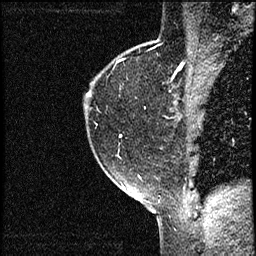
Breast MRI (dynamic contrast-enhanced), one sagittal slice. Slice 44 of 56 in the series (ordered by position). Dynamic contrast-enhanced study with each time point stored as its own series, time point 2 of 3 at this slice position (early post-contrast, ordered by acquisition time). 1.5 T. TE 4.2 ms, TR 17.3 ms. 2 mm slice thickness. 256 × 256 image matrix, field of view 200 × 200 mm. Female patient. From the clinical record (not read from this slice): setting: breast cancer imaged before/during neoadjuvant chemotherapy; receptor status: HER2-positive.
Outlined on this slice (semi-automatically segmented with operator editing):
- analysis volume of interest (the breast-tissue region the enhancement analysis was run in; not a lesion): bounding box (x1, y1, x2, y2) in pixels: (83, 50, 136, 155)
- tumour enhancement mask (voxels above the 100 % enhancement threshold inside the analysis volume of interest): (119, 136, 121, 138)